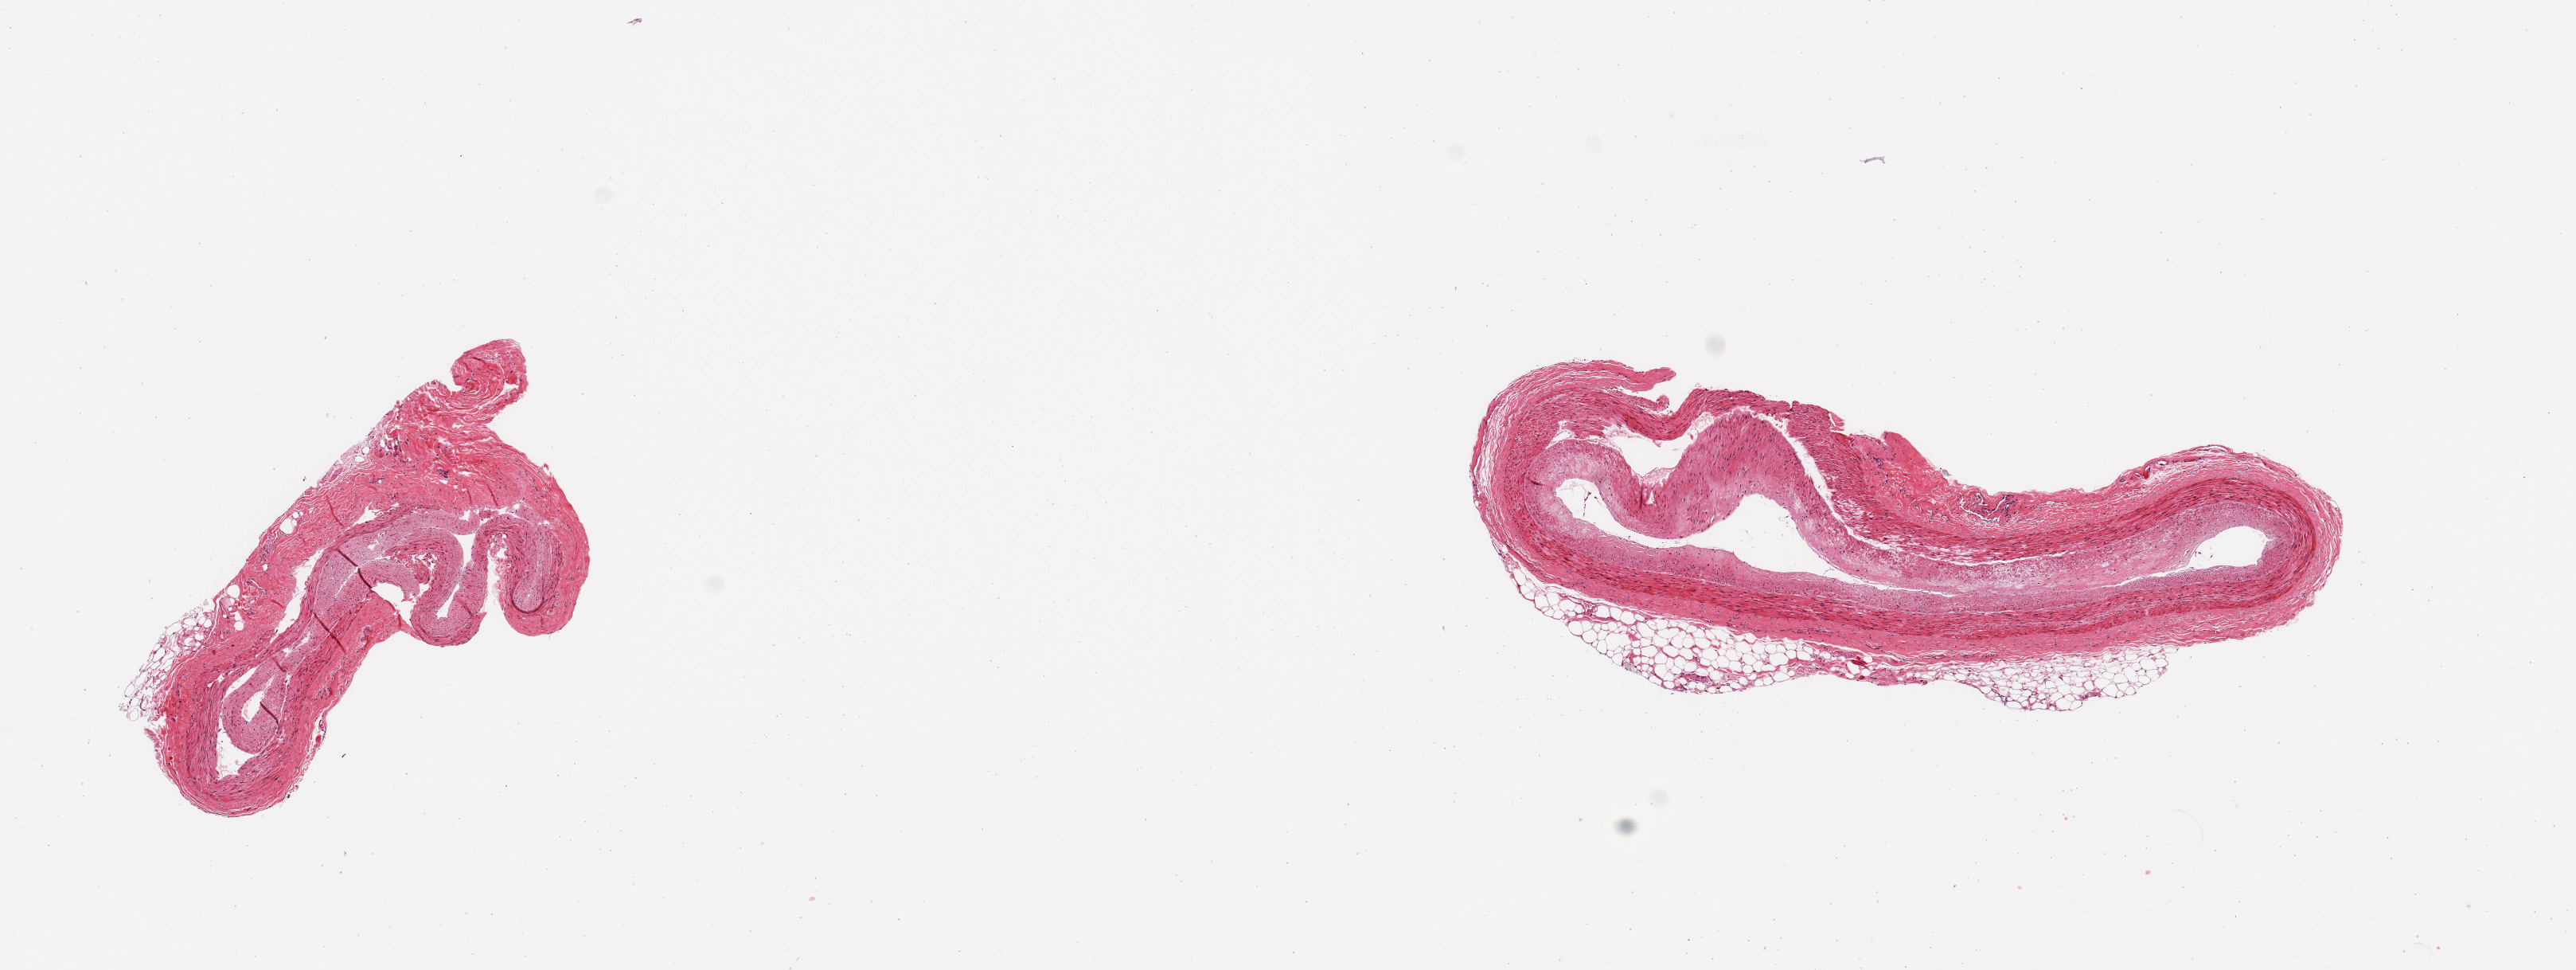
Digitized hematoxylin and eosin (H&E)-stained section, shown as a low-resolution overview of the whole scanned area (about 12.8 x 4.8 mm, acquisition: 20x scan), PAXgene-fixed paraffin-embedded (PFPE) section, sampled site (target tissue): coronary artery, donor tissue sample. Donor: female.
Pathologist's review note for this sample: 2 pieces; minimal plaque; 10% external fat.